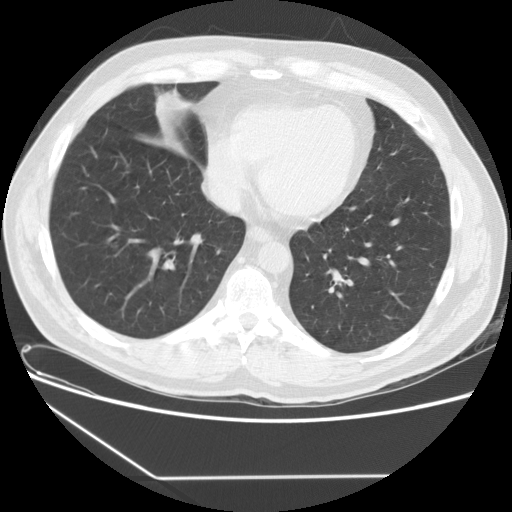
Chest CT (low-dose screening protocol), one axial image. Baseline annual screen. Lung window (W 1500 / L -600 HU). Slice 105 of 154 in the series. 512 × 512 image matrix, field of view 370 × 370 mm. Male participant, aged 59 years at enrolment. Current smoker at enrolment.
Expert-annotated lung lesion, bounding box (x1, y1, x2, y2) in pixels: (149, 86, 198, 118). No non-calcified nodule or mass ≥4 mm was recorded by the screening reader at this exam. Lung cancer was diagnosed 58 days after this screen: oat cell carcinoma, right middle lobe, stage IIA (AJCC 6th edition), 15 mm at pathology.